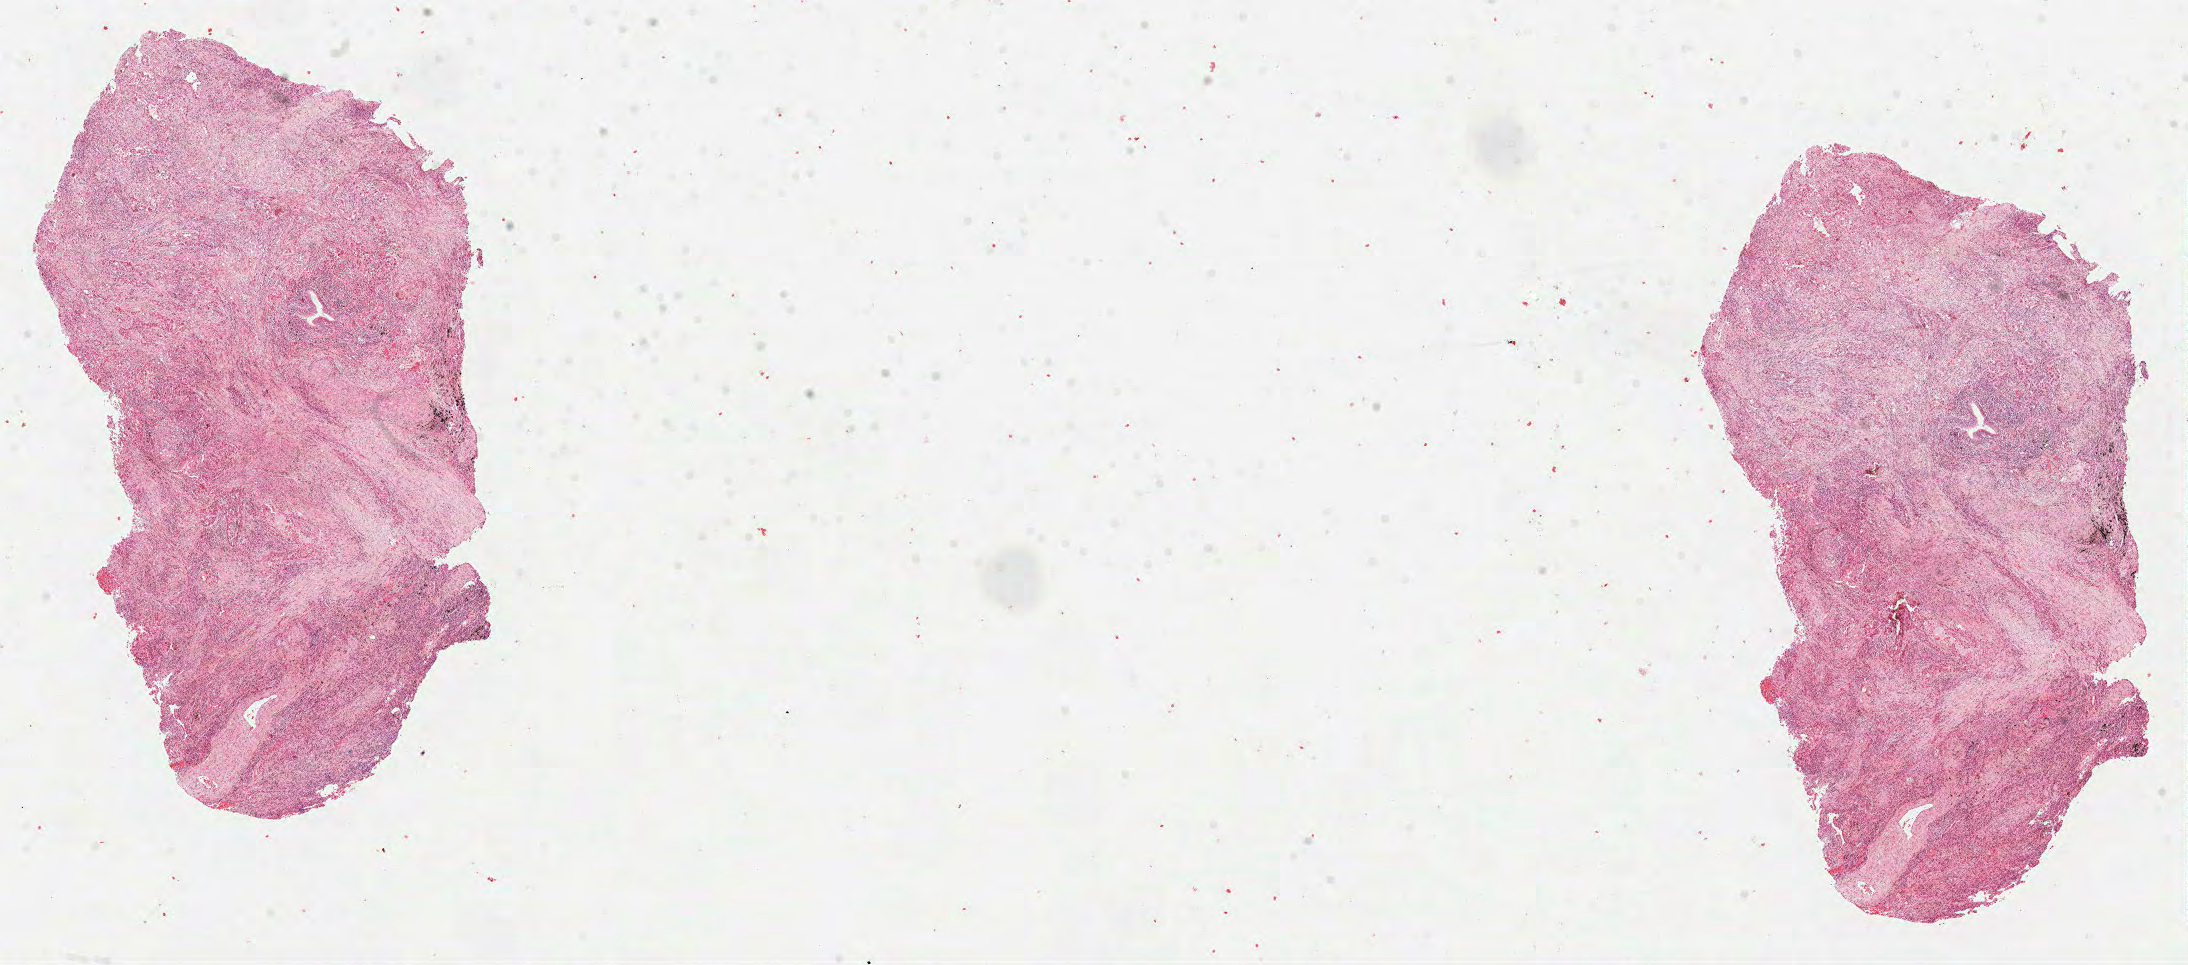
Whole-slide histology image, H&E, shown as a low-resolution overview of the whole scanned area (about 17.6 x 7.8 mm, from a 40x scan), formalin-fixed paraffin-embedded (FFPE) diagnostic section, sample: primary tumour, lung. Female, age 50 years at initial diagnosis.
TNM: T1a N0 M0. AJCC pathologic stage: IA (7th edition). Histologic diagnosis: Adenocarcinoma, NOS.